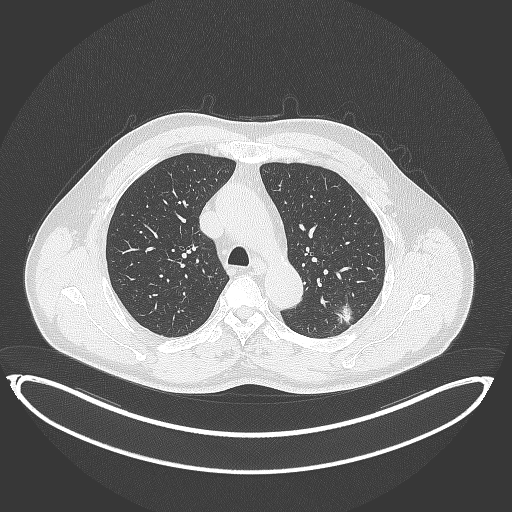
Chest CT, one axial slice; slice 257 of 399 in the series (ordered by position); reconstruction kernel B70f; 120 kVp; lung window (W 1500 / L -600 HU); 1 mm slice thickness; 512 × 512 image matrix. Patient: male, 58 years. From the clinical record (not read from this slice): clinical TNM (as recorded): T1c N0 M0; histopathological grade: G1-2.
Annotated regions visible in this slice (rectangle marked by the reading radiologist):
- lung tumour (recorded histology: adenocarcinoma): box from (x=328, y=297) to (x=359, y=328) px